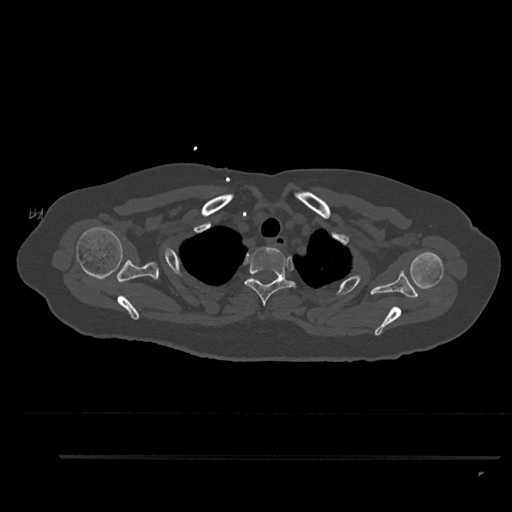
CT including the spine, one axial slice; position 723 of 797 along the scan axis; reconstruction kernel Br40s/3; 120 kVp; bone window (W 1800 / L 400 HU); 0.5 mm slice thickness; 512 × 512 image matrix. Female patient, age 44 years. From the clinical record (not read from this slice): primary cancer: renal.
Outlined on this slice (semi-automatic segmentation, software-assisted and operator-edited):
- T2 vertebra: bounding box <244,247,296,306> (left, top, right, bottom; pixels)